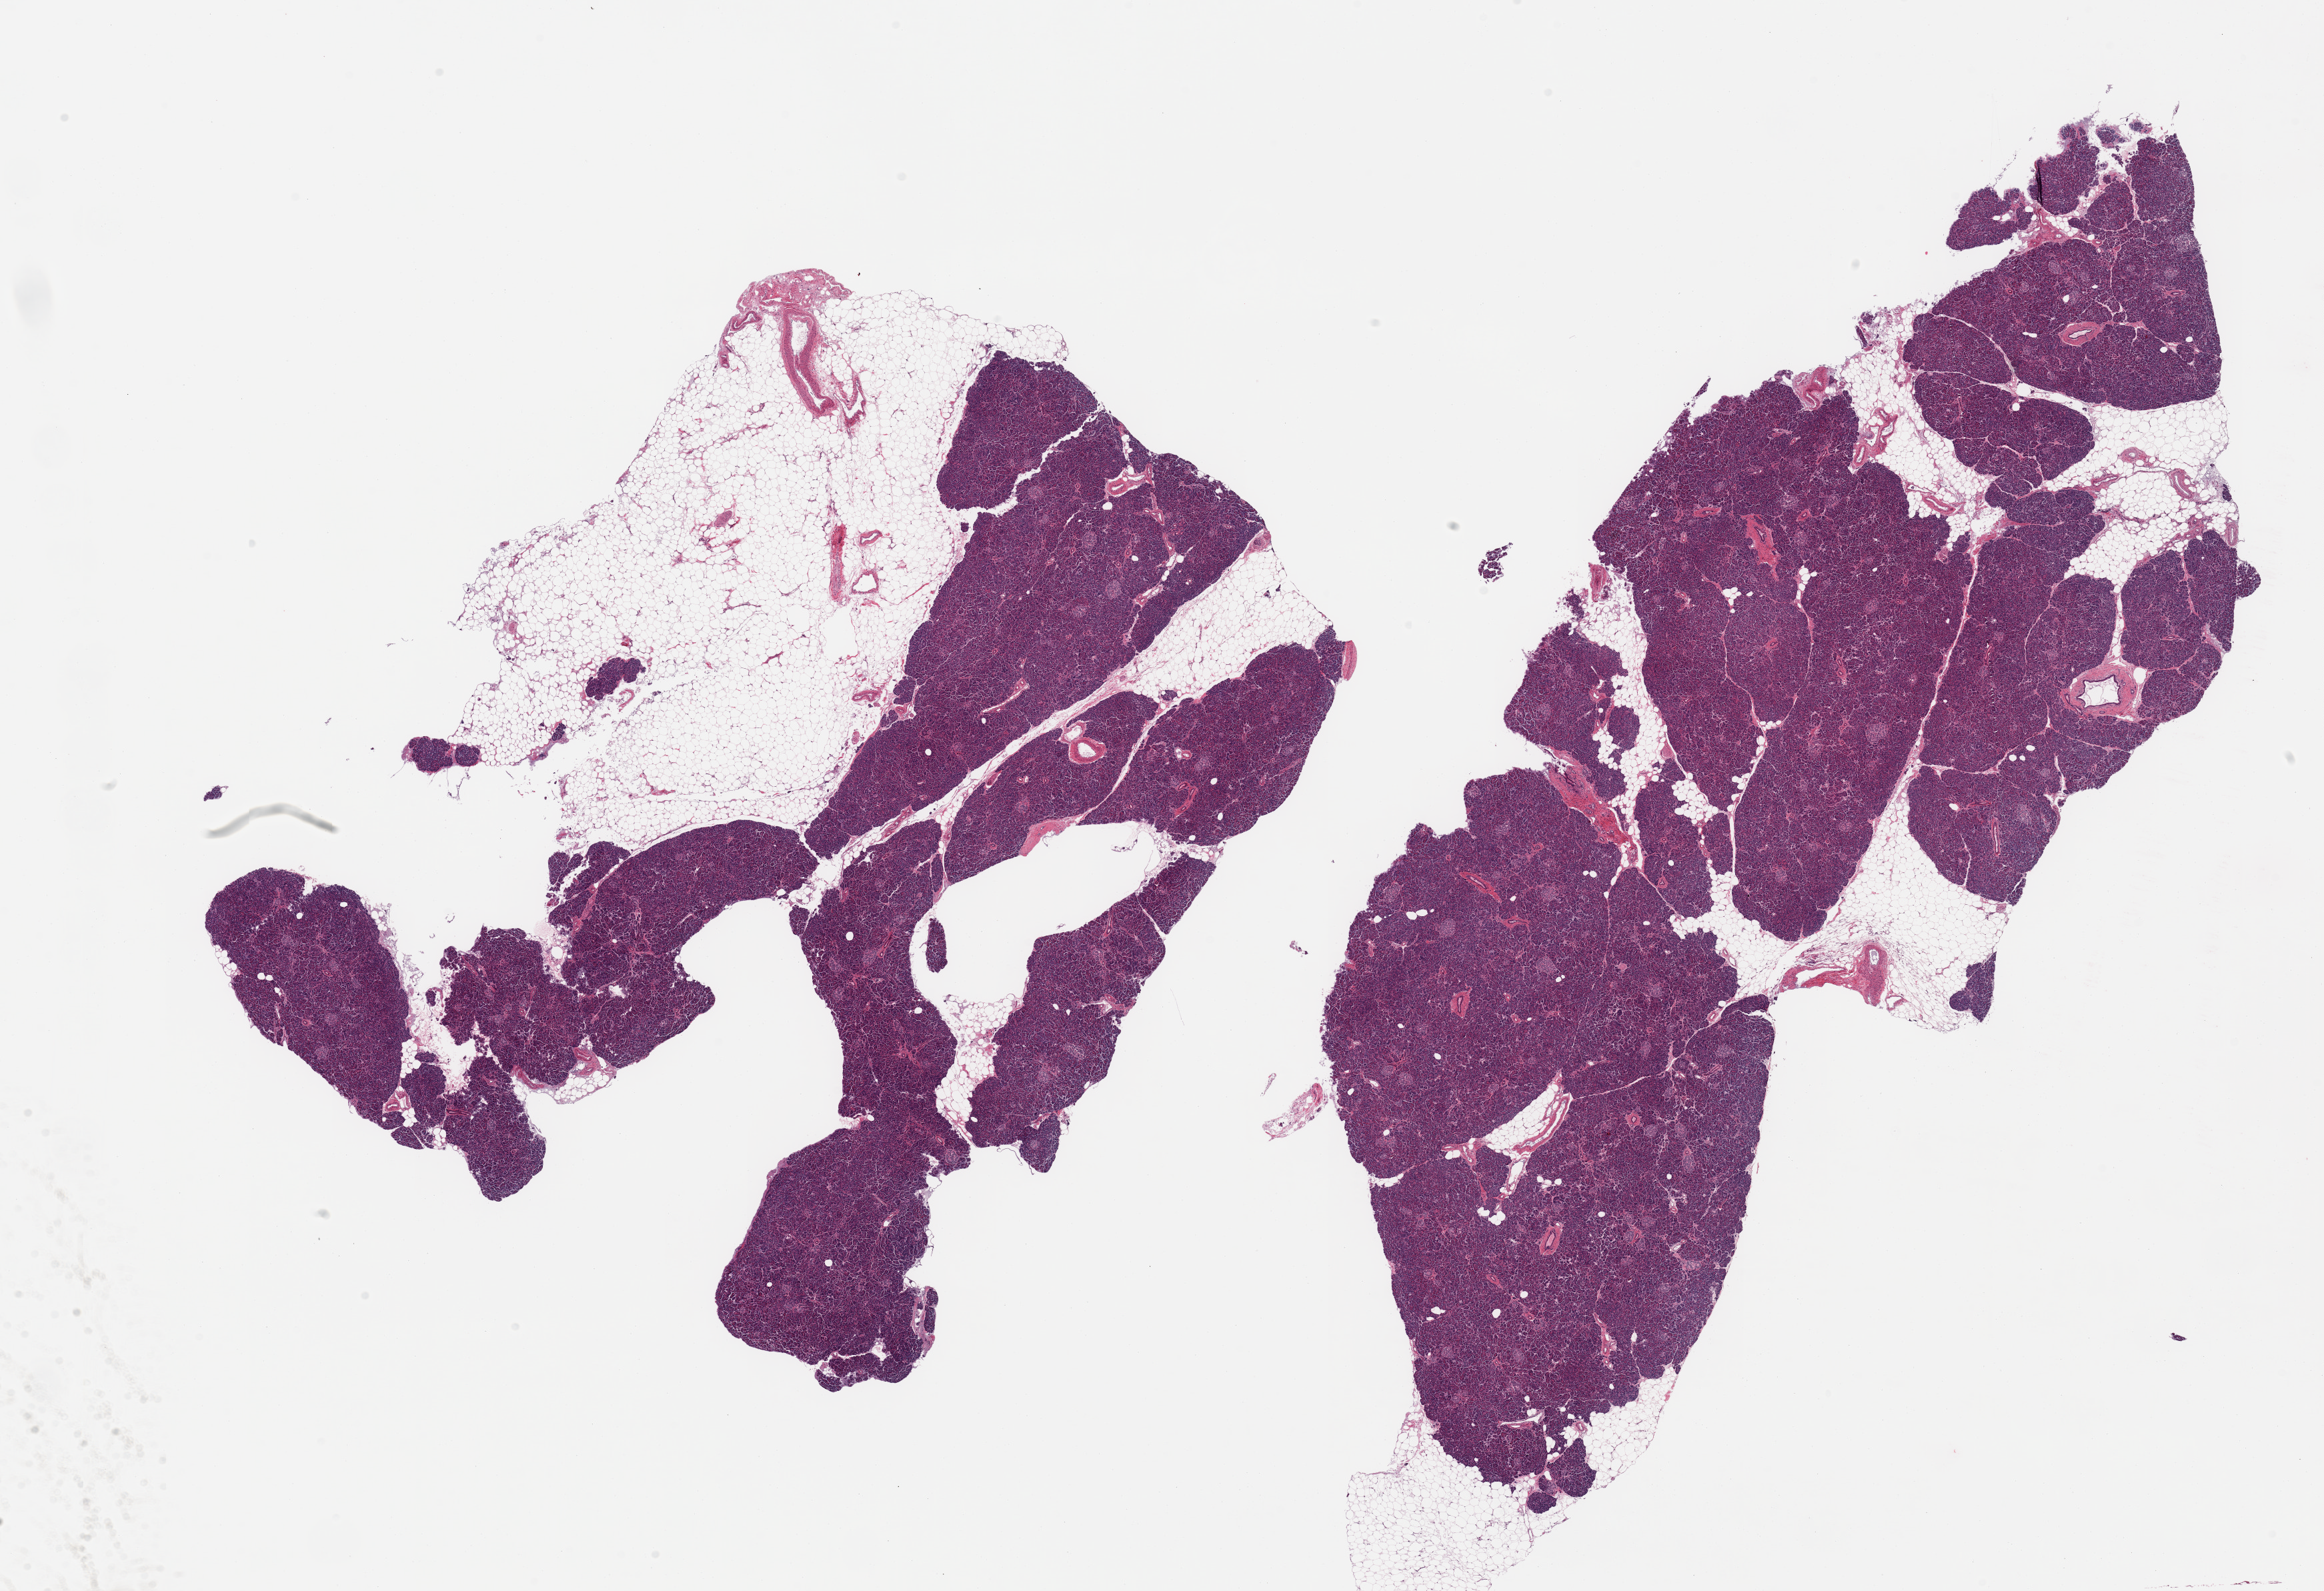
Whole-slide image, haematoxylin and eosin stain, whole scanned area (about 27.6 x 18.9 mm, from a 20x scan) shown as a low-resolution overview, PAXgene-fixed paraffin-embedded (PFPE) section, target tissue: pancreas, donor tissue sample. Donor: male.
Reviewer comment on this tissue sample: 2 pieces; from 10-50% fat, mild autolysis and interstitial fibrosis, numerous well preserved islets.